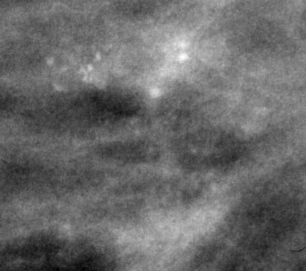
Crop from a digitized film mammogram around one marked abnormality, left breast, MLO view.
- Finding: calcifications, morphology pleomorphic, distribution clustered; BI-RADS assessment category 4; pathology result (as recorded, not read from the image): malignant.